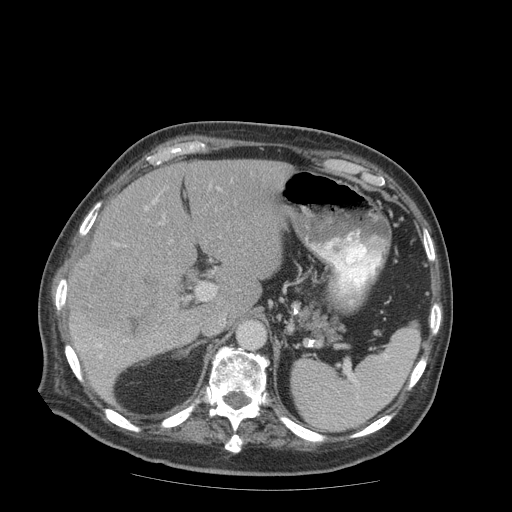
Contrast-enhanced abdominal CT (liver protocol), one axial slice. Slice 54 of 99 in the series (ordered by position). 140 kVp. Soft-tissue window (W 400 / L 40 HU). 512 × 512 image matrix, field of view 420 × 420 mm. From the clinical record (not read from this slice): diagnosis: hepatocellular carcinoma (patient treated with transarterial chemoembolisation; whether this scan precedes or follows treatment is not stated here); TNM stage (as recorded): Stage-IIIB; Child-Pugh class: A; tumour differentiation: well differentiated; tumour nodularity: multinodular.
Annotated regions visible in this slice (semi-automatic segmentation, software-assisted and operator-edited):
- liver parenchyma outside the tumour (the mass and vessels are separate outlines, so this box may not span the whole liver): bounding box [x1, y1, x2, y2] px = [66, 160, 292, 400]
- mass: [69, 247, 179, 348]
- liver vessels: [99, 187, 220, 359]